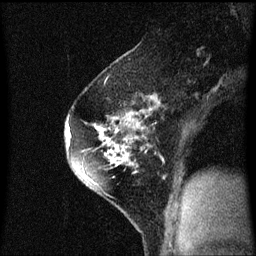
Breast MRI (dynamic contrast-enhanced), one sagittal slice; position 40 of 60 along the scan axis; dynamic contrast-enhanced series, image 2 of 3 at this slice position (ordered by acquisition); 1.5 T; TE 4.2 ms, TR 8.4 ms; 256 × 256 image matrix. Patient: female, 60 years.
Outlined on this slice (semi-automatic segmentation, software-assisted and operator-edited):
- analysis volume of interest (the breast-tissue region the enhancement analysis was run in; not a lesion): bounding box <64,70,147,195> (left, top, right, bottom; pixels)
- tumour enhancement mask (voxels above the 70 % enhancement threshold inside the analysis volume of interest): <66,110,145,183>